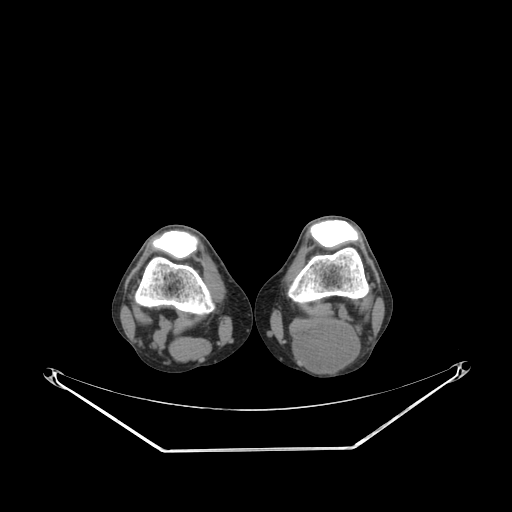
CT of an extremity soft-tissue mass (from a PET/CT study), one axial slice; slice 184 of 267 in the series (ordered by position); reconstruction kernel SOFT; 140 kVp; soft-tissue window (W 400 / L 40 HU); 3.75 mm slice thickness; 512 × 512 image matrix, field of view 500 × 500 mm. Male patient. Case-level facts recorded for this patient, not image findings: histological type: synovial sarcoma; site of the primary tumour: left poplietal fossa.
Structures marked on this image (expert contour drawn on MRI and transferred to this co-registered scan by the dataset authors):
- gross tumour volume (mass): bounding box [x1, y1, x2, y2] px = [290, 322, 362, 373]